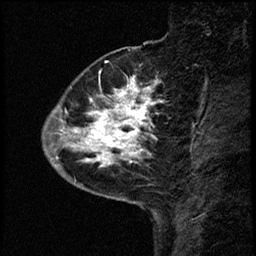
Breast MRI (dynamic contrast-enhanced), one sagittal slice. Position 15 of 68 along the scan axis. Dynamic contrast-enhanced study with each time point stored as its own series, time point 2 of 3 at this slice position (early post-contrast, ordered by acquisition time). 1.5 T. TE 4.2 ms, TR 17.6 ms. 2 mm slice thickness. 256 × 256 image matrix, field of view 200 × 200 mm. Patient: female, 52 years. Case-level facts recorded for this patient, not image findings: setting: breast cancer imaged before/during neoadjuvant chemotherapy; receptor status: HER2-positive.
Structures marked on this image (semi-automatically segmented with operator editing):
- analysis volume of interest (the breast-tissue region the enhancement analysis was run in; not a lesion): bounding box (x1, y1, x2, y2) in pixels: (50, 61, 161, 184)
- tumour enhancement mask (voxels above the 100 % enhancement threshold inside the analysis volume of interest): (56, 78, 157, 168)